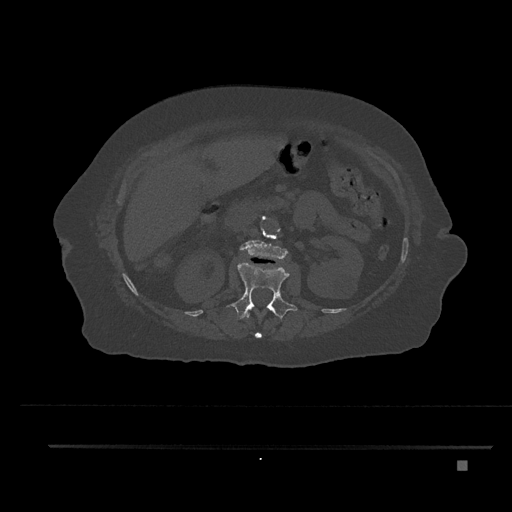
CT including the spine, one axial slice; slice 219 of 797 in the series (ordered by position); 120 kVp; bone window (W 1800 / L 400 HU); 512 × 512 image matrix, field of view 437 × 437 mm. Female patient, age 76 years. From the clinical record (not read from this slice): primary cancer: lung.
Annotated regions visible in this slice (semi-automatically segmented with operator editing):
- L1 vertebra: bounding box (x1, y1, x2, y2) in pixels: (233, 262, 297, 321)
- L2 vertebra: (240, 240, 288, 260)
- T12 vertebra: (245, 311, 276, 339)